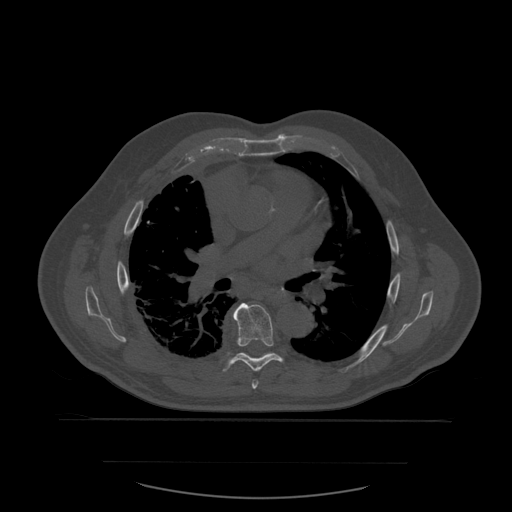
CT including the spine, one axial slice. Position 383 of 590 along the scan axis. Bone window (W 1800 / L 400 HU). 512 × 512 image matrix, field of view 479 × 479 mm. Patient age 71 years. From the clinical record (not read from this slice): primary cancer: lung; vertebrae with lytic lesions (as recorded): T1, T2, L5, S1.
Annotated regions visible in this slice (semi-automatically segmented with operator editing):
- T6 vertebra: bounding box (x1, y1, x2, y2) in pixels: (252, 380, 259, 389)
- T7 vertebra: (223, 303, 283, 372)